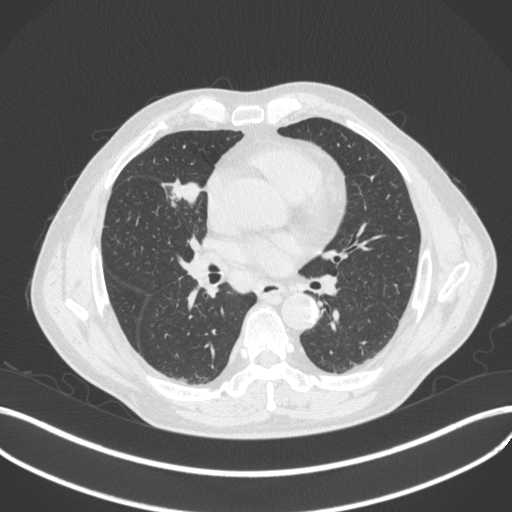
Chest CT, one axial slice; position 203 of 429 along the scan axis; reconstruction kernel B31f; 120 kVp; lung window (W 1500 / L -600 HU); 512 × 512 image matrix, field of view 400 × 400 mm. Male patient, age 61 years. From the clinical record (not read from this slice): clinical TNM (as recorded): T2b N1 M0.
Annotated regions visible in this slice (rectangle marked by the reading radiologist):
- lung tumour (recorded histology: squamous cell carcinoma): box from (x=162, y=174) to (x=202, y=204) px